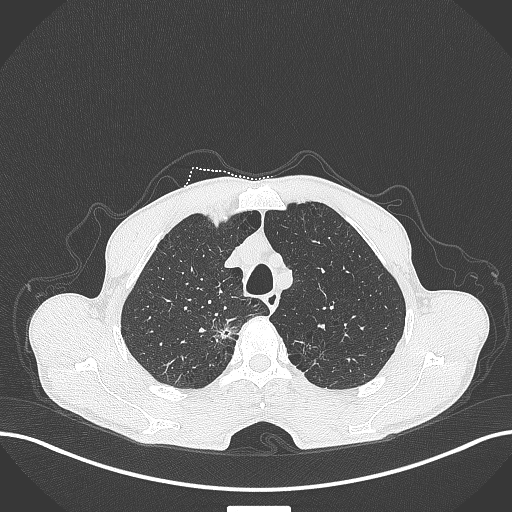
Chest CT, one axial slice; slice 346 of 445 in the series (ordered by position); reconstruction kernel B70f; 120 kVp; lung window (W 1500 / L -600 HU); 512 × 512 image matrix, field of view 400 × 400 mm. Male patient, age 70 years. From the clinical record (not read from this slice): clinical TNM (as recorded): T1a N0 M0; histopathological grade: G1-2.
Outlined on this slice (bounding box drawn by a radiologist):
- lung tumour (recorded histology: adenocarcinoma): bounding box [x1, y1, x2, y2] px = [214, 323, 240, 346]